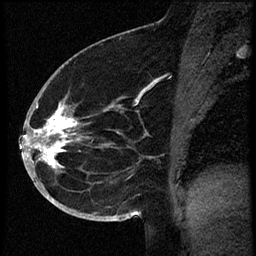
Breast MRI (dynamic contrast-enhanced), one sagittal slice; slice 34 of 60 in the series (ordered by position); dynamic contrast-enhanced study with each time point stored as its own series, time point 2 of 3 at this slice position (early post-contrast, ordered by acquisition time); 1.5 T; TE 4.2 ms, TR 18.9 ms; 256 × 256 image matrix, field of view 200 × 200 mm. Female patient. From the clinical record (not read from this slice): setting: breast cancer imaged before/during neoadjuvant chemotherapy; receptor status: HR-positive, HER2-negative.
Annotated regions visible in this slice (semi-automatic segmentation, software-assisted and operator-edited):
- analysis volume of interest (the breast-tissue region the enhancement analysis was run in; not a lesion): bounding box <30,87,114,173> (left, top, right, bottom; pixels)
- tumour enhancement mask (voxels above the 100 % enhancement threshold inside the analysis volume of interest): <30,104,78,168>